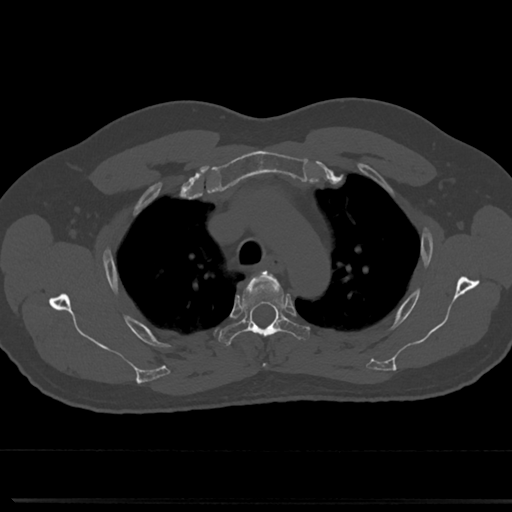
CT including the spine, one axial slice; slice 557 of 817 in the series (ordered by position); reconstruction kernel Br40s/3; bone window (W 1800 / L 400 HU); 512 × 512 image matrix, field of view 355 × 355 mm. Male patient, age 61 years. From the clinical record (not read from this slice): primary cancer: prostate.
Annotated regions visible in this slice (semi-automatic segmentation, software-assisted and operator-edited):
- T3 vertebra: bounding box [x1, y1, x2, y2] px = [264, 363, 268, 367]
- T4 vertebra: [219, 271, 310, 344]